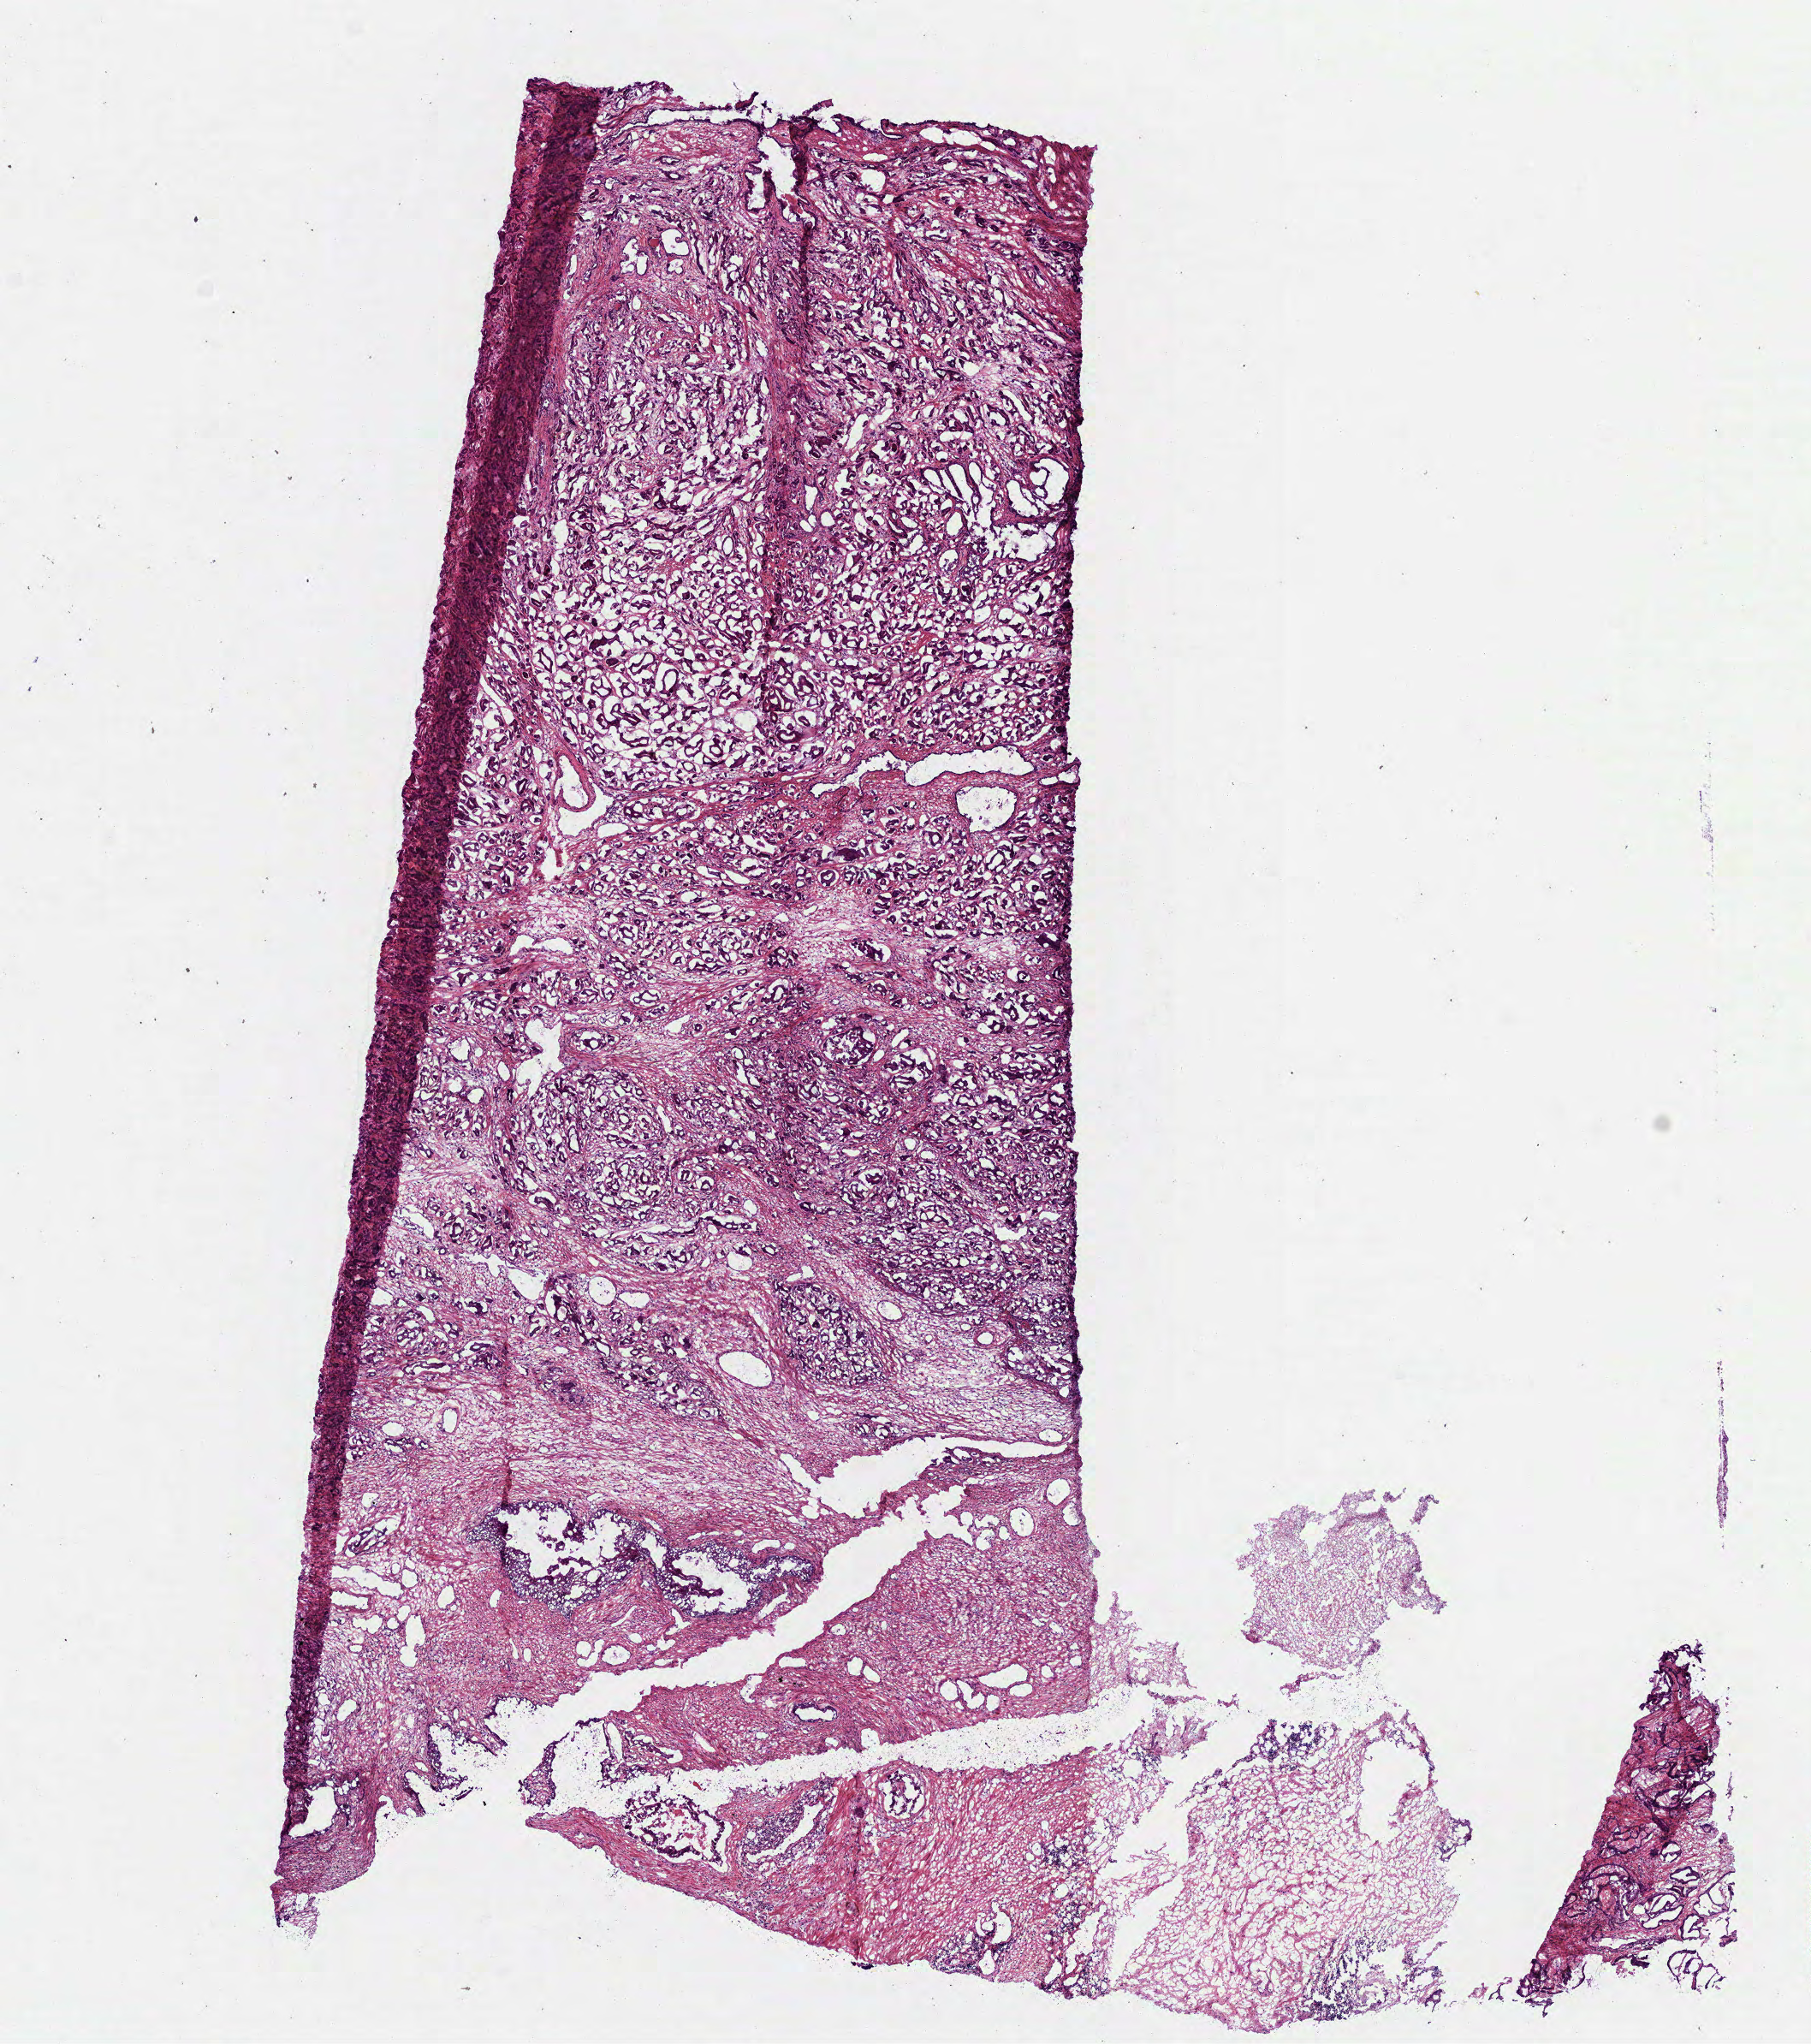
H&E whole-slide image, shown as a low-resolution overview of the whole scanned area (about 8.5 x 9.6 mm), frozen section, primary tumour sample from the prostate. Patient: male, age at initial diagnosis 64 years. Gleason score: 7 (4+3). Pathologist review of this section (percent, as recorded): tumour cells 65%, tumour nuclei 70%, normal cells 10%, stromal cells 25%, necrosis 0%. Inflammatory infiltration, as recorded: lymphocyte infiltration 5%, monocyte infiltration 2%, neutrophil infiltration 0%.
Diagnosis: Acinar cell carcinoma (prostate gland). Lymph nodes positive (case pathology): 0 of 6 examined.